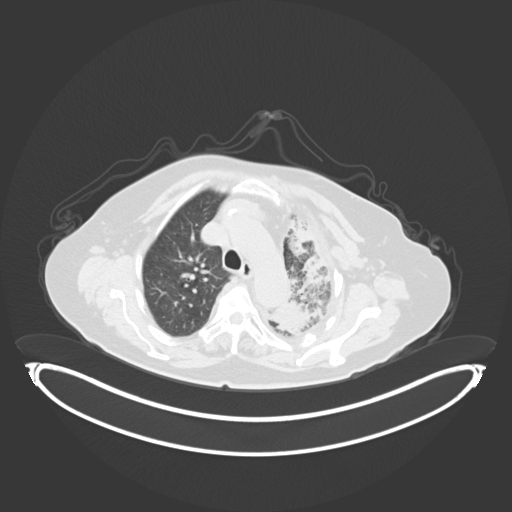
Chest CT, one axial slice. Position 219 of 284 along the scan axis. 120 kVp. Lung window (W 1500 / L -600 HU). 512 × 512 image matrix. Patient: female, 75 years. Case-level facts recorded for this patient, not image findings: clinical TNM (as recorded): T3 N3 M1.
Outlined on this slice (rectangle marked by the reading radiologist):
- lung tumour (recorded histology: adenocarcinoma): bounding box (x1, y1, x2, y2) in pixels: (265, 213, 334, 337)